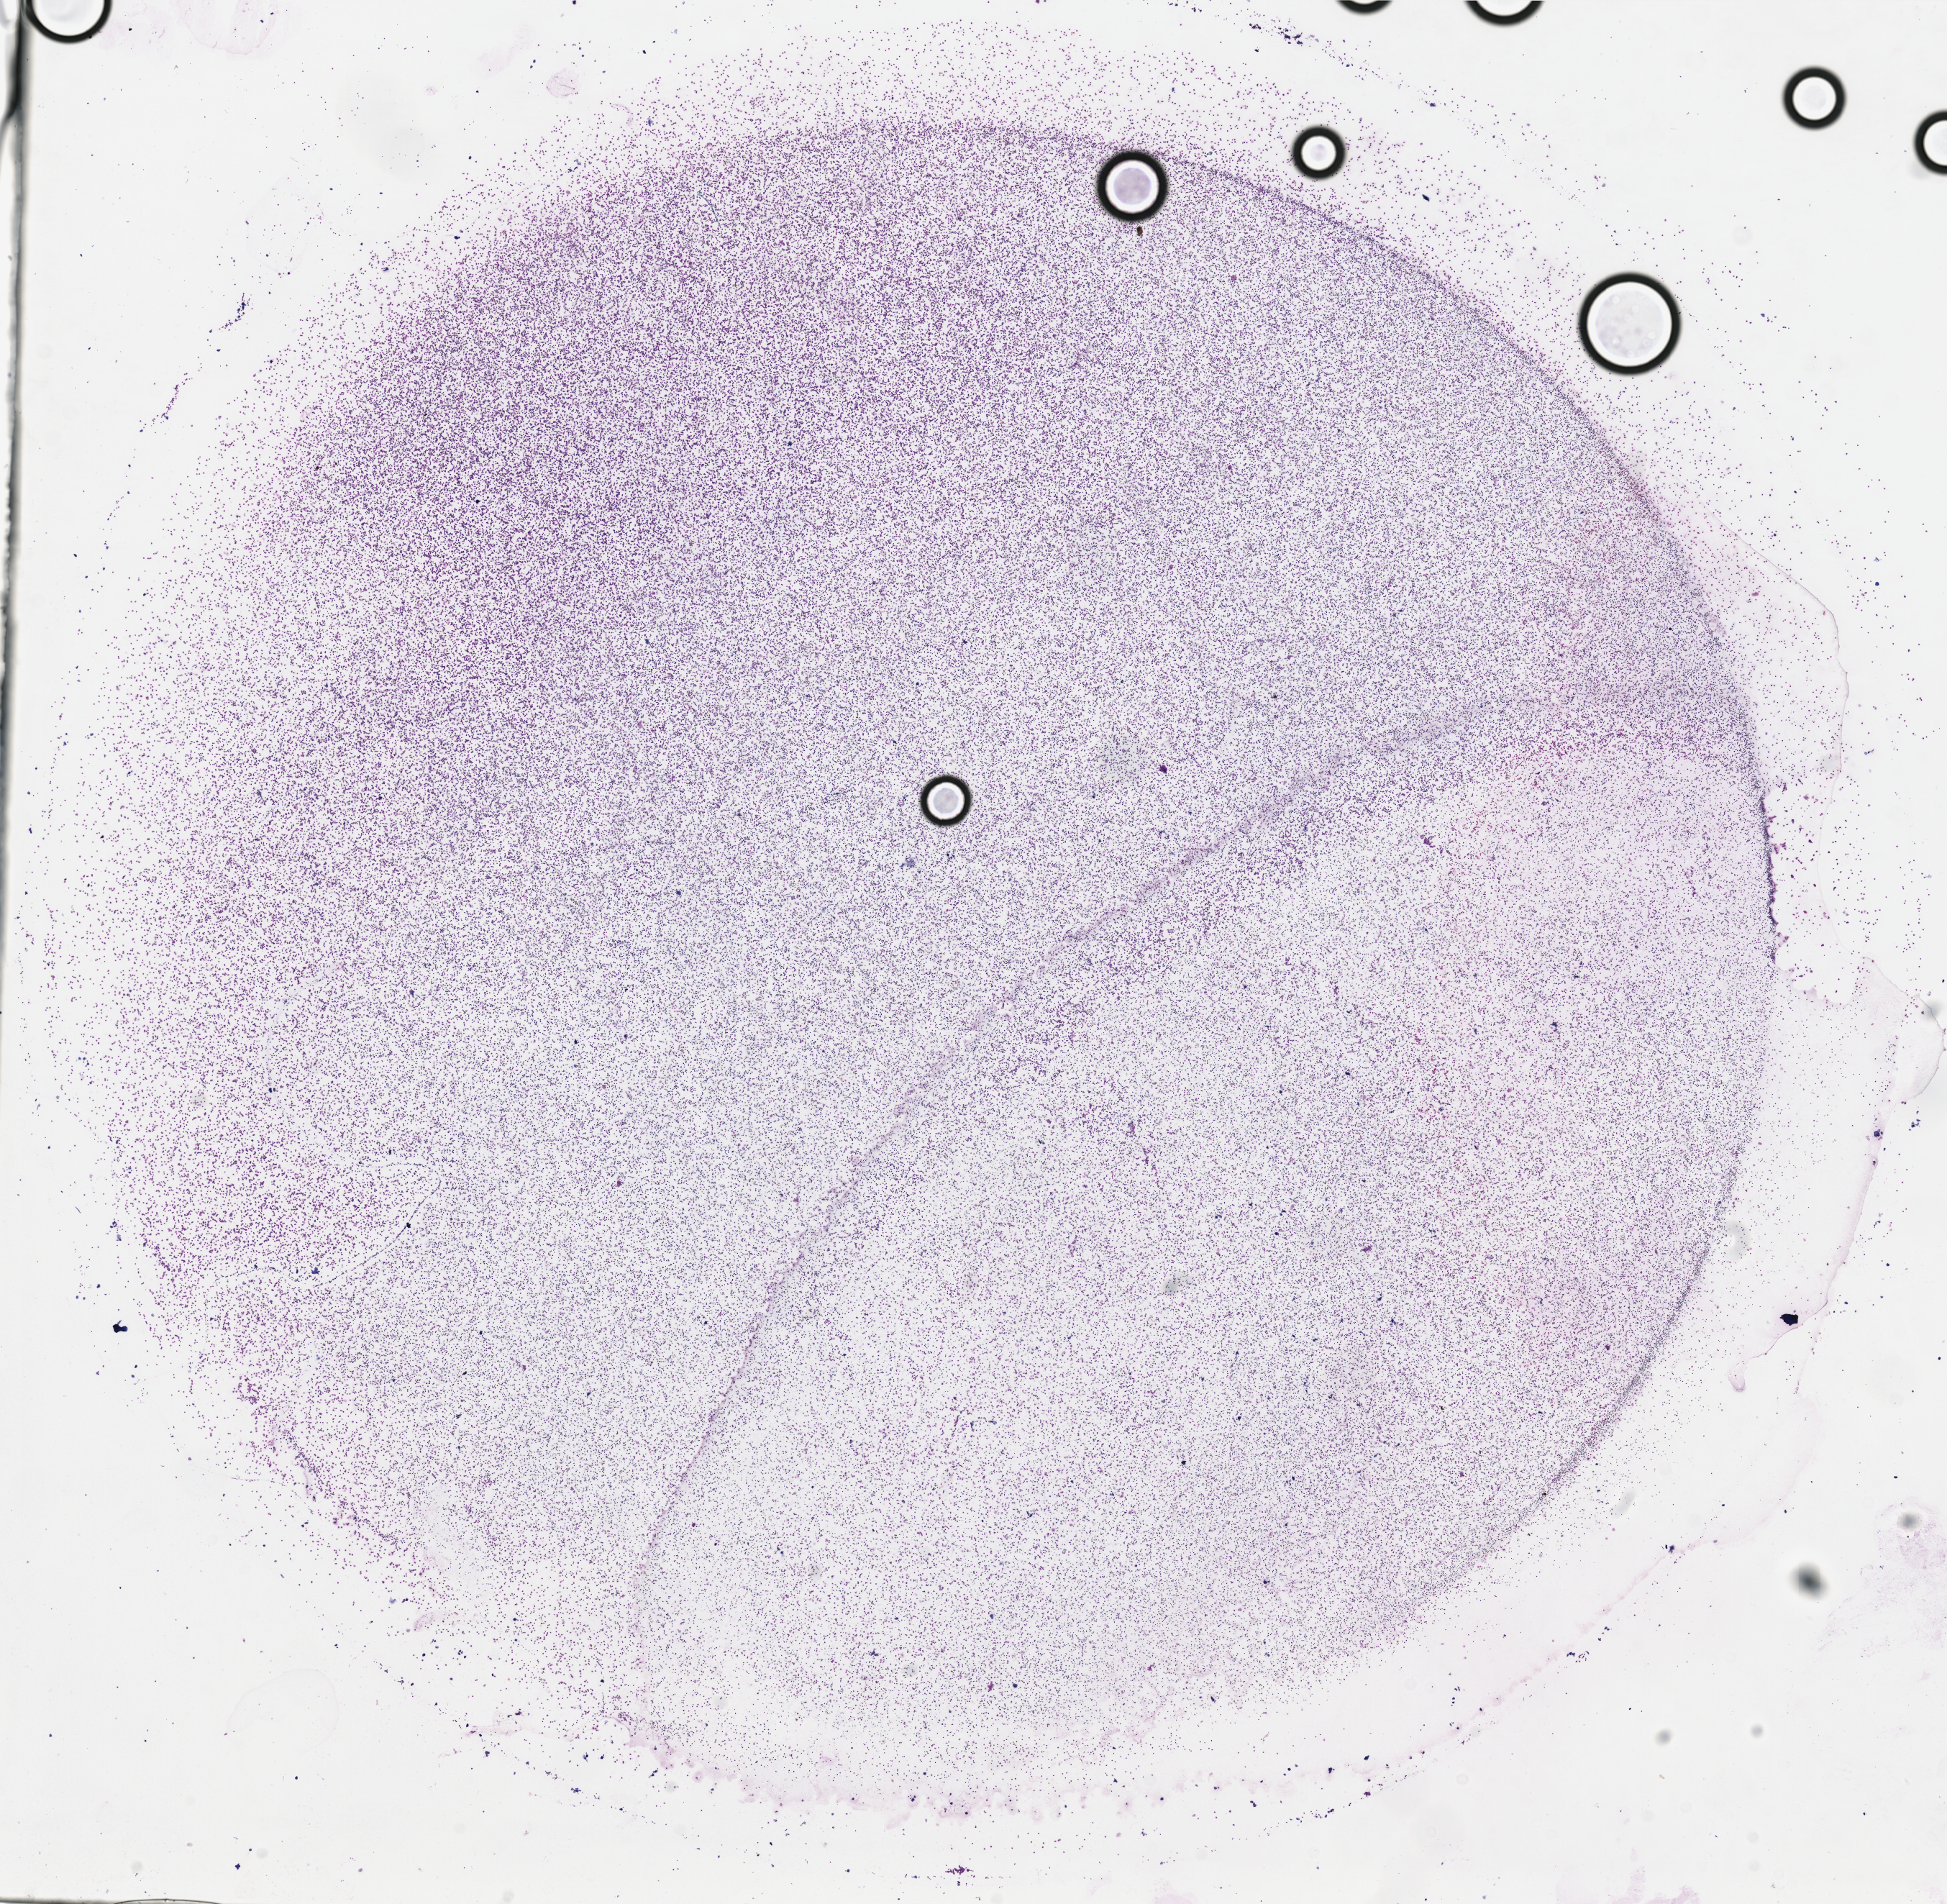
H&E whole-slide image, whole scanned area (about 21.4 x 20.9 mm, acquisition: 40x scan) shown as a low-resolution overview; bone marrow (leukaemic) sample. Patient: male, age 40 years.
Diagnosis: Acute Myeloid Leukemia.